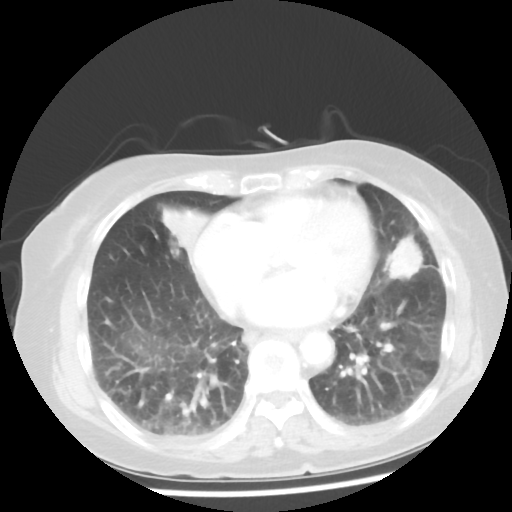
Chest CT, one axial slice; position 16 of 50 along the scan axis; reconstruction kernel STANDARD; 100 kVp; lung window (W 1500 / L -600 HU); 512 × 512 image matrix, field of view 332 × 332 mm. Patient: female, 77 years. Case-level facts recorded for this patient, not image findings: clinical TNM (as recorded): T2 N3 M1a.
Annotated regions visible in this slice (bounding box drawn by a radiologist):
- lung tumour (recorded histology: adenocarcinoma): box from (x=380, y=228) to (x=428, y=284) px